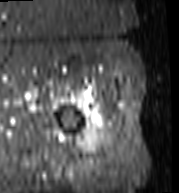
MRI of an extremity soft-tissue mass, one axial slice; position 93 of 103 along the scan axis; STIR; MR volume resampled by the dataset authors to the PET/CT grid (not the native acquisition matrix); 3.27 mm slice thickness; 179 × 193 image matrix, field of view 175 × 188 mm. Female patient. From the clinical record (not read from this slice): histological type: undifferentiated – high grade; grade: high; site of the primary tumour: left thigh.
Outlined on this slice (expert contour drawn on MRI and transferred to this co-registered scan by the dataset authors):
- gross tumour volume including surrounding oedema: bounding box (x1, y1, x2, y2) in pixels: (75, 101, 108, 154)
- gross tumour volume (mass): (86, 131, 99, 136)